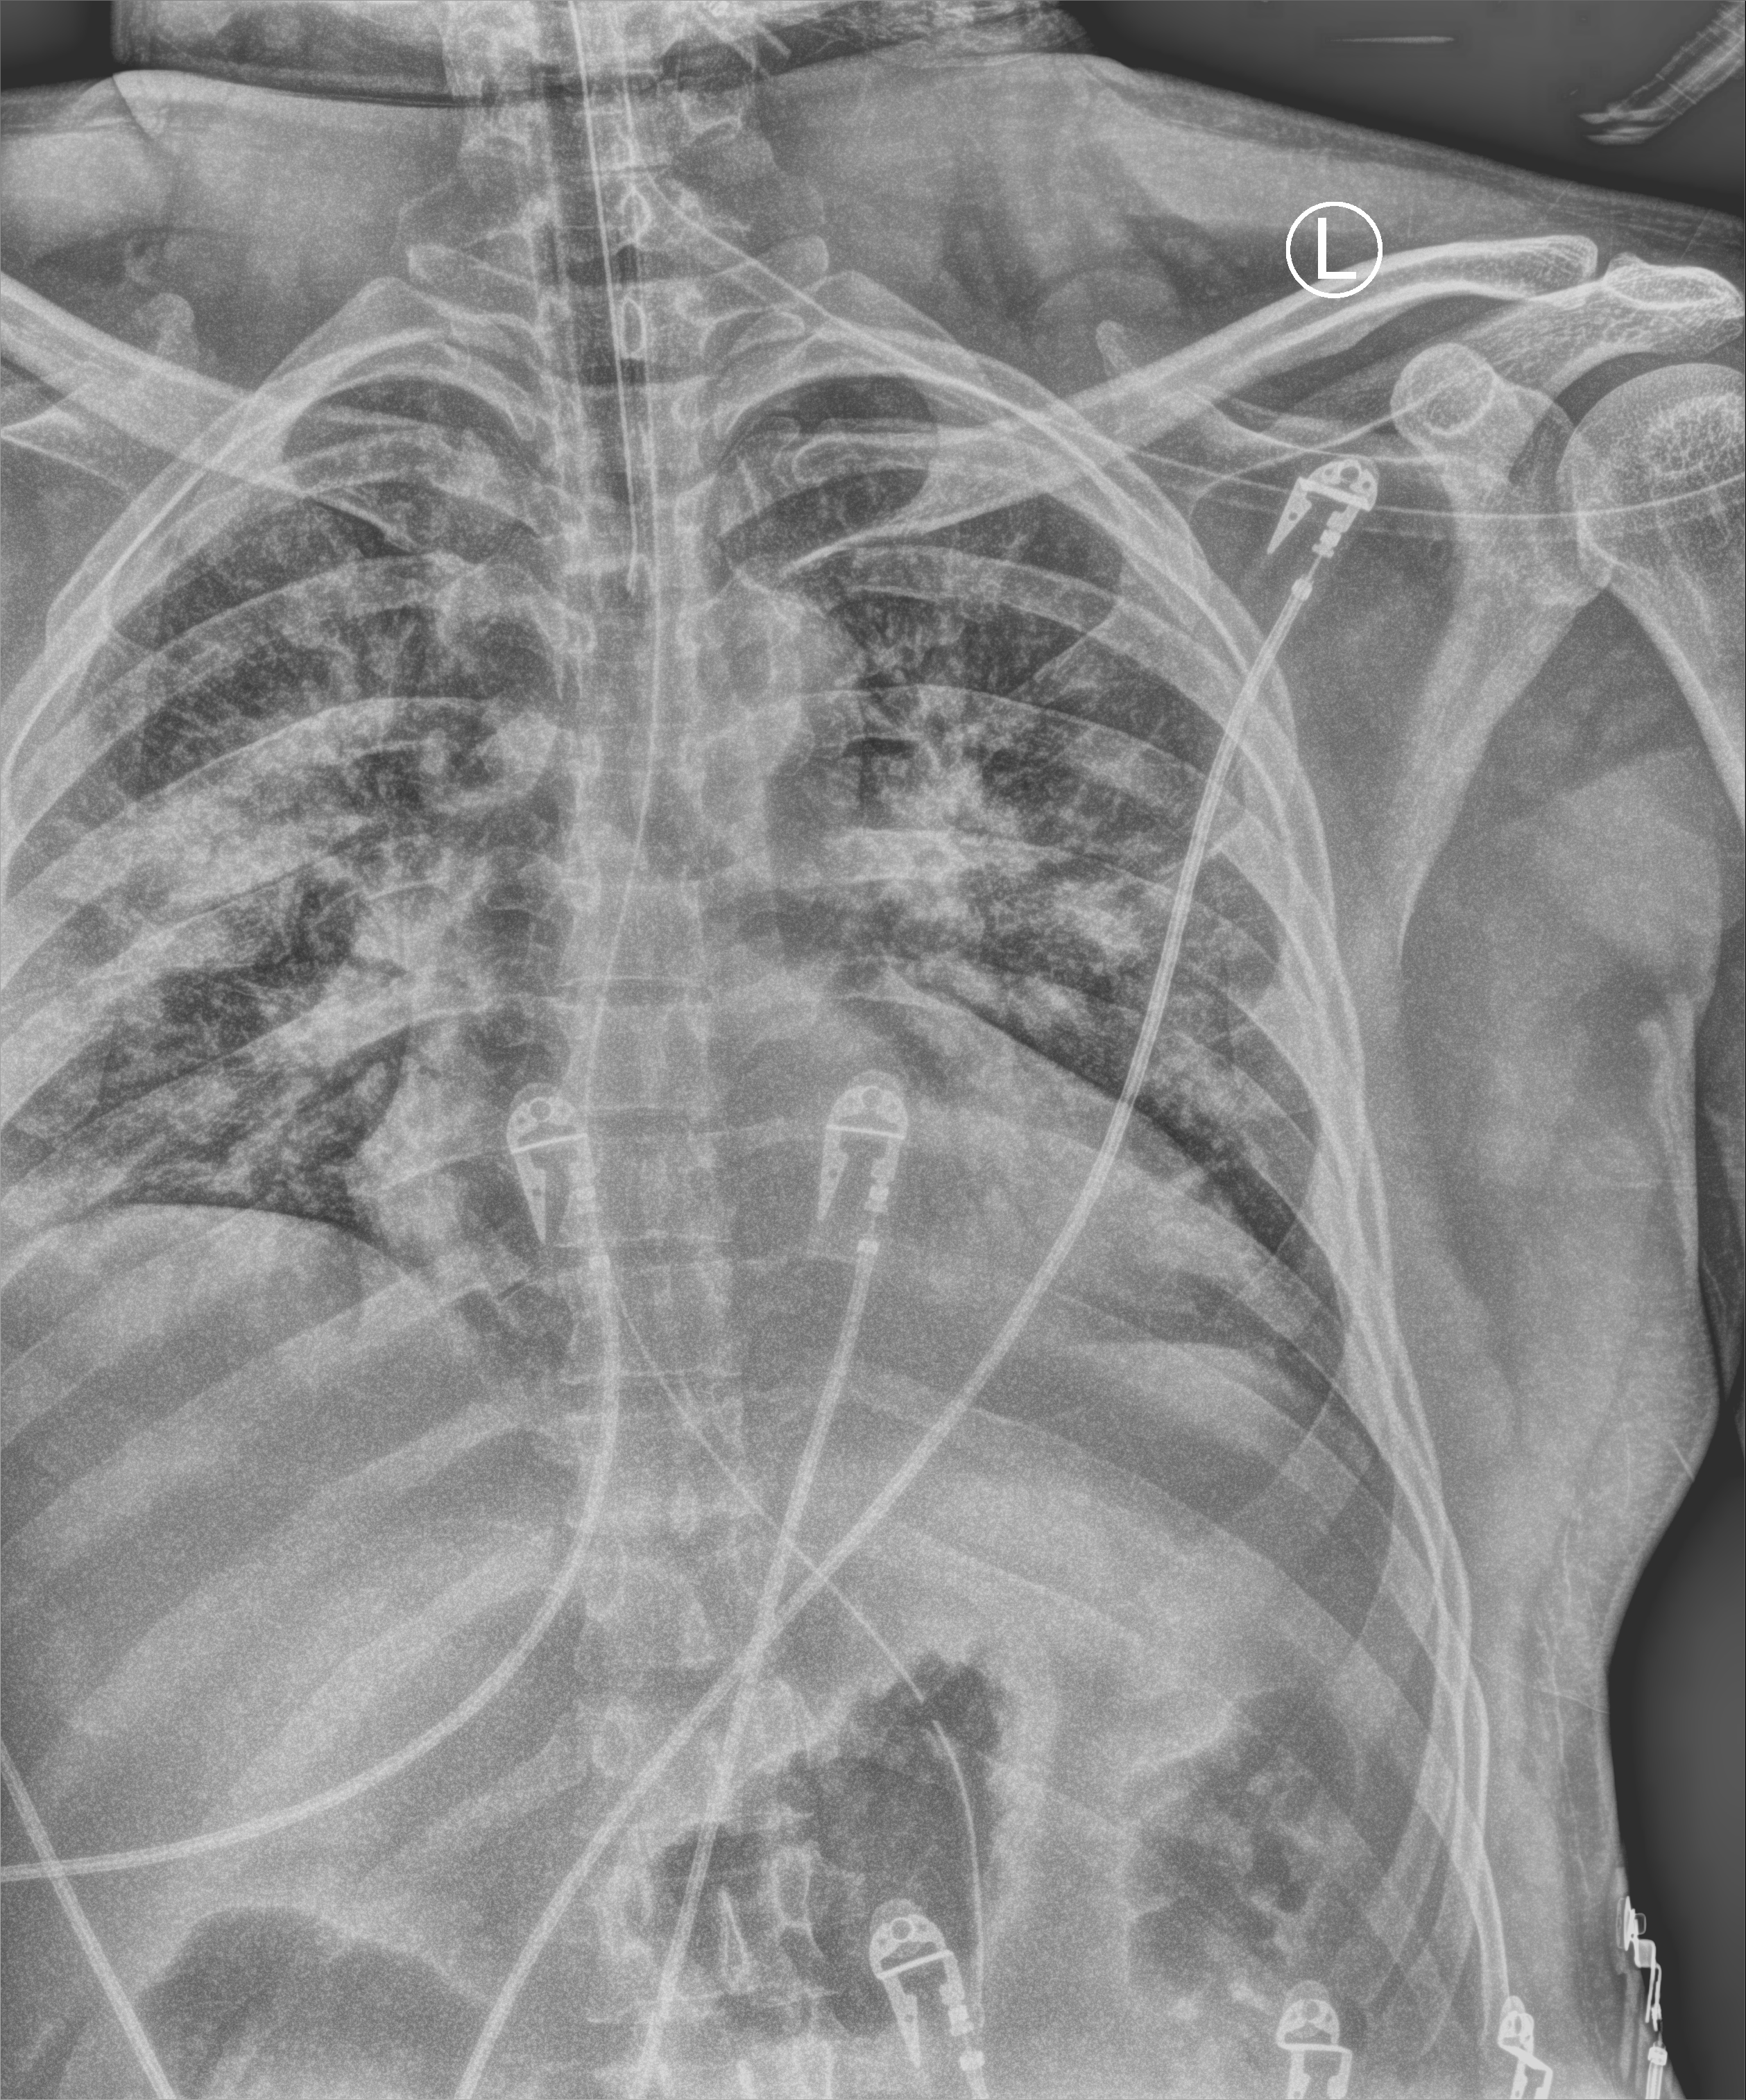
Bedside chest radiograph (computed radiography), anteroposterior (AP) projection. Male patient hospitalised with COVID-19, age 18–59 years.
Hospital-stay facts (about this admission, not read from this image; timing relative to this image not recorded): admitted to intensive care during this hospital stay: yes; mechanically ventilated during this hospital stay: yes.